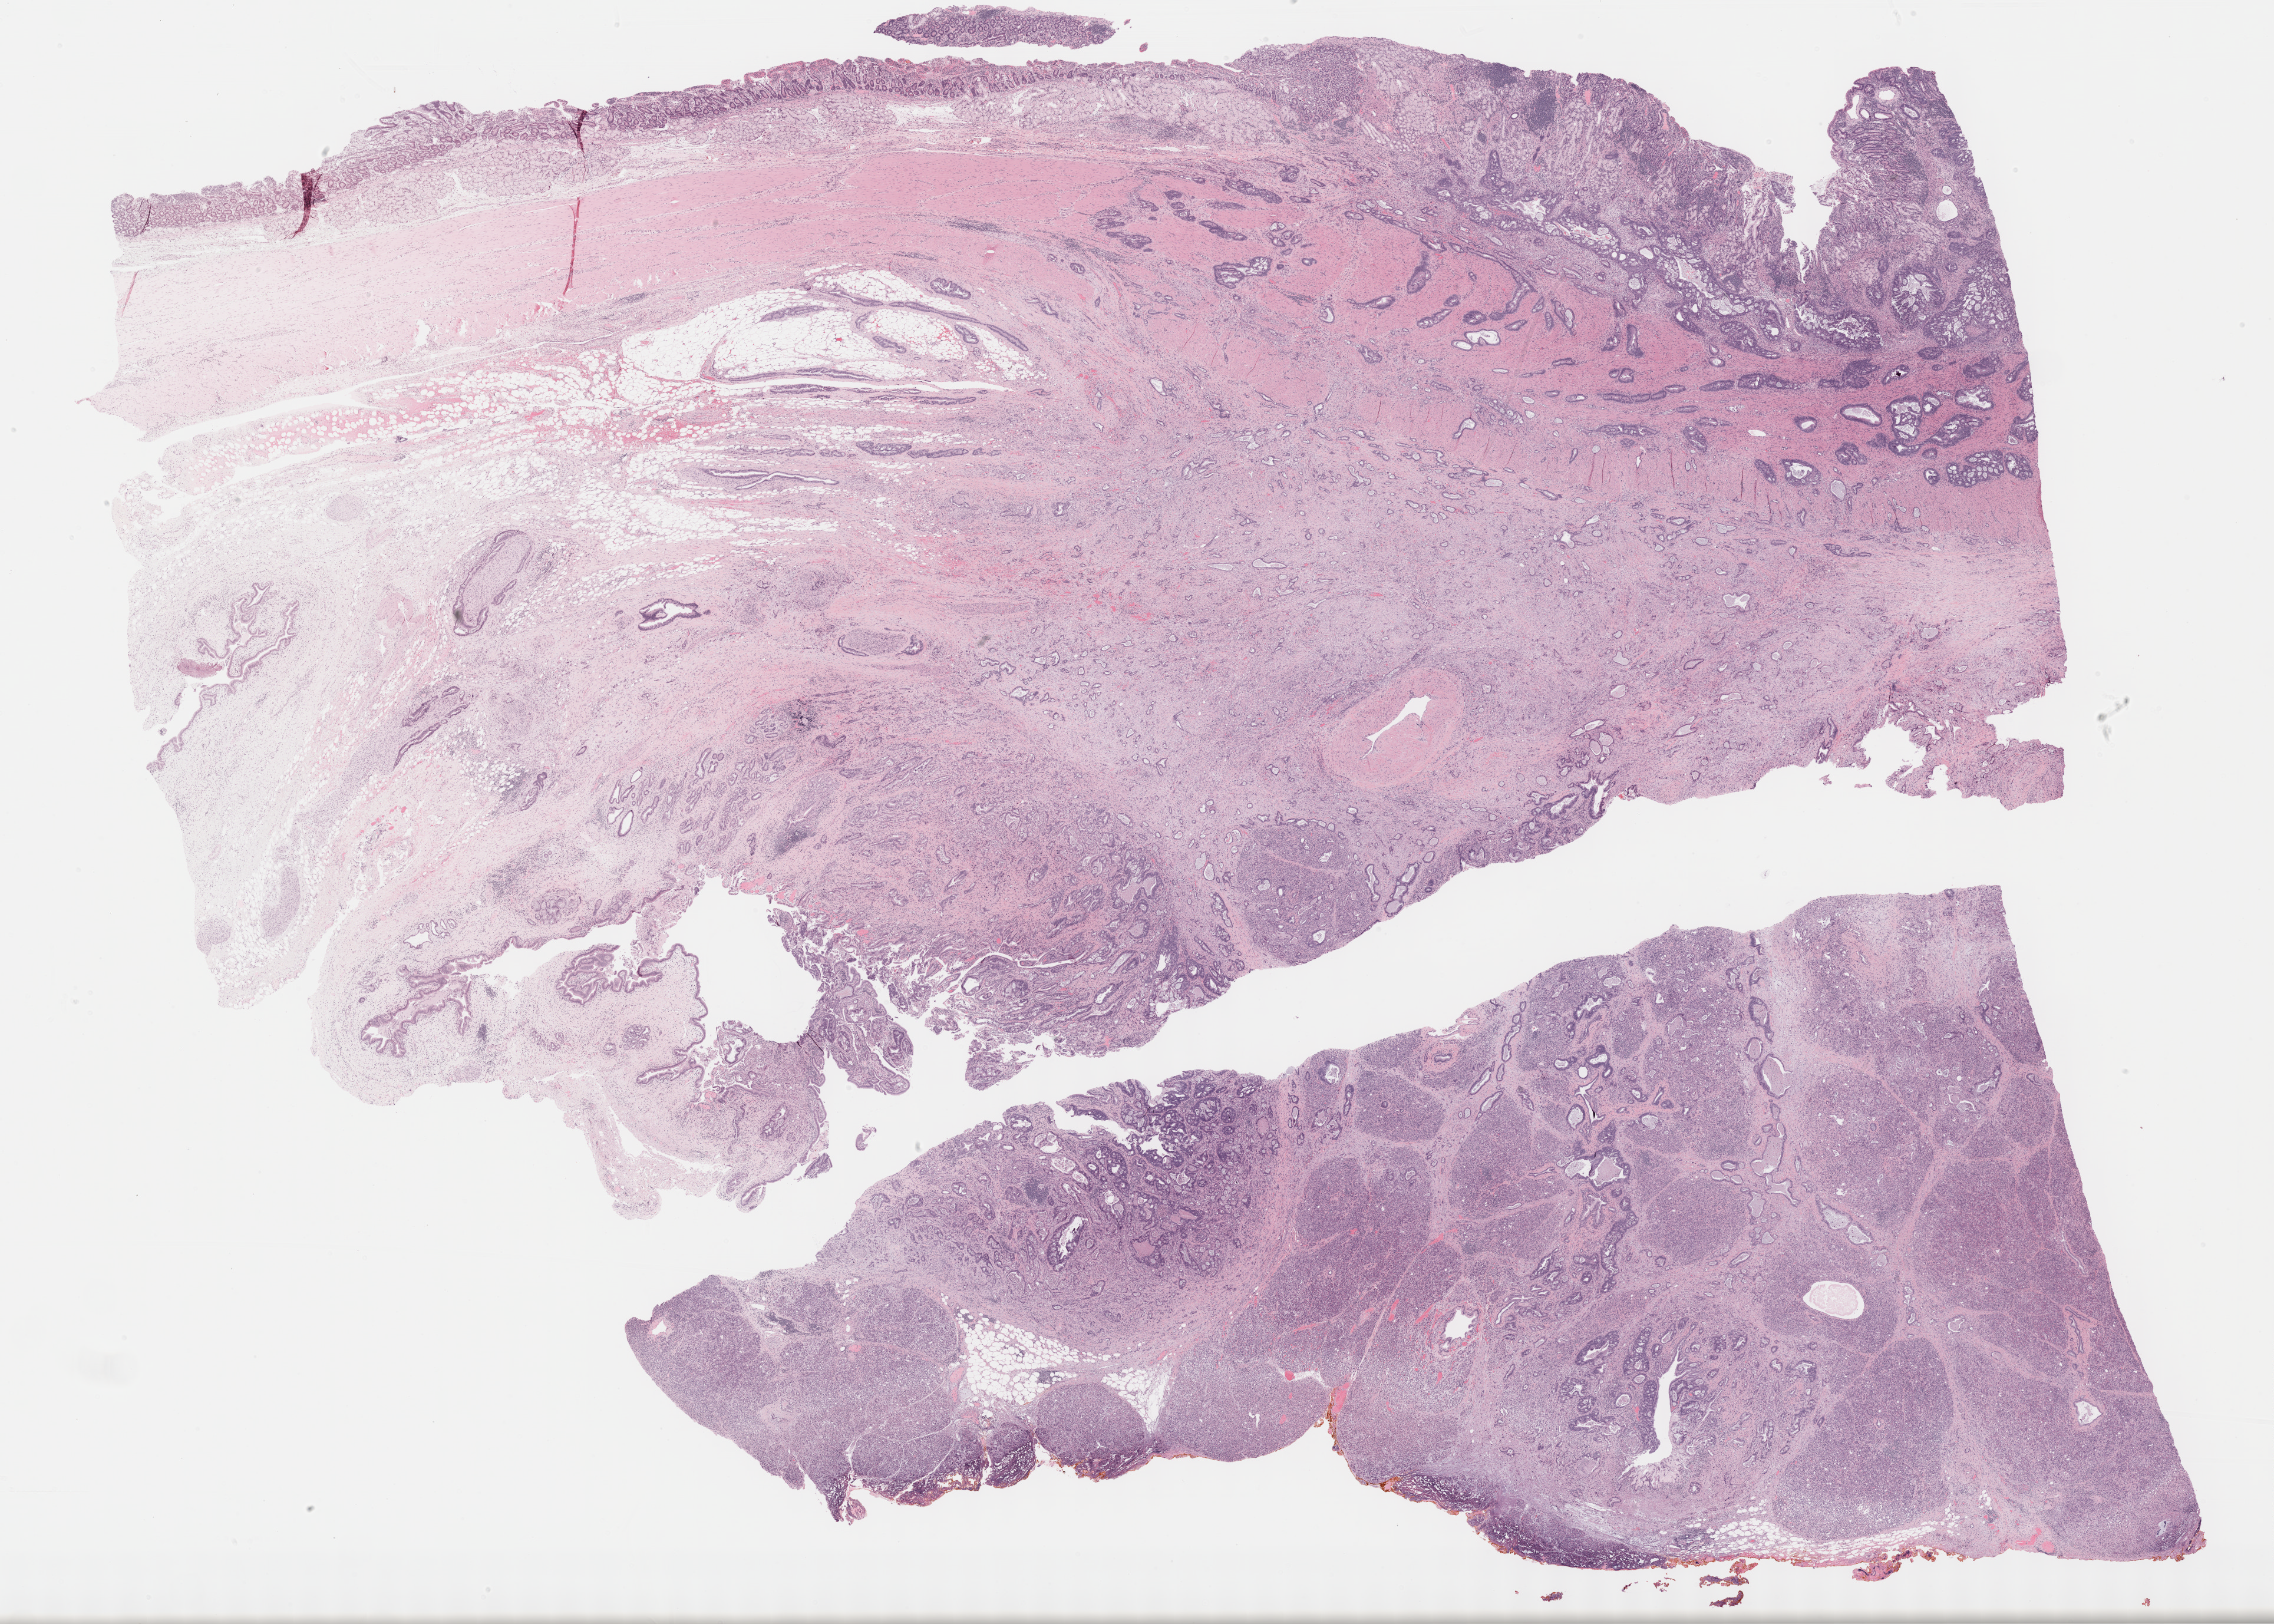
Hematoxylin and eosin (H&E) stained whole-slide image, shown as a low-resolution overview of the whole scanned area (about 31.2 x 22.3 mm); formalin-fixed paraffin-embedded (FFPE) diagnostic section; sample: primary tumour, pancreas. Patient: male, age at initial diagnosis 80 years. Histologic grade: G3 (poorly differentiated).
- TNM: T3 N1 M0
- AJCC pathologic stage: IIB (7th edition)
- pathologic diagnosis: Infiltrating duct carcinoma, NOS